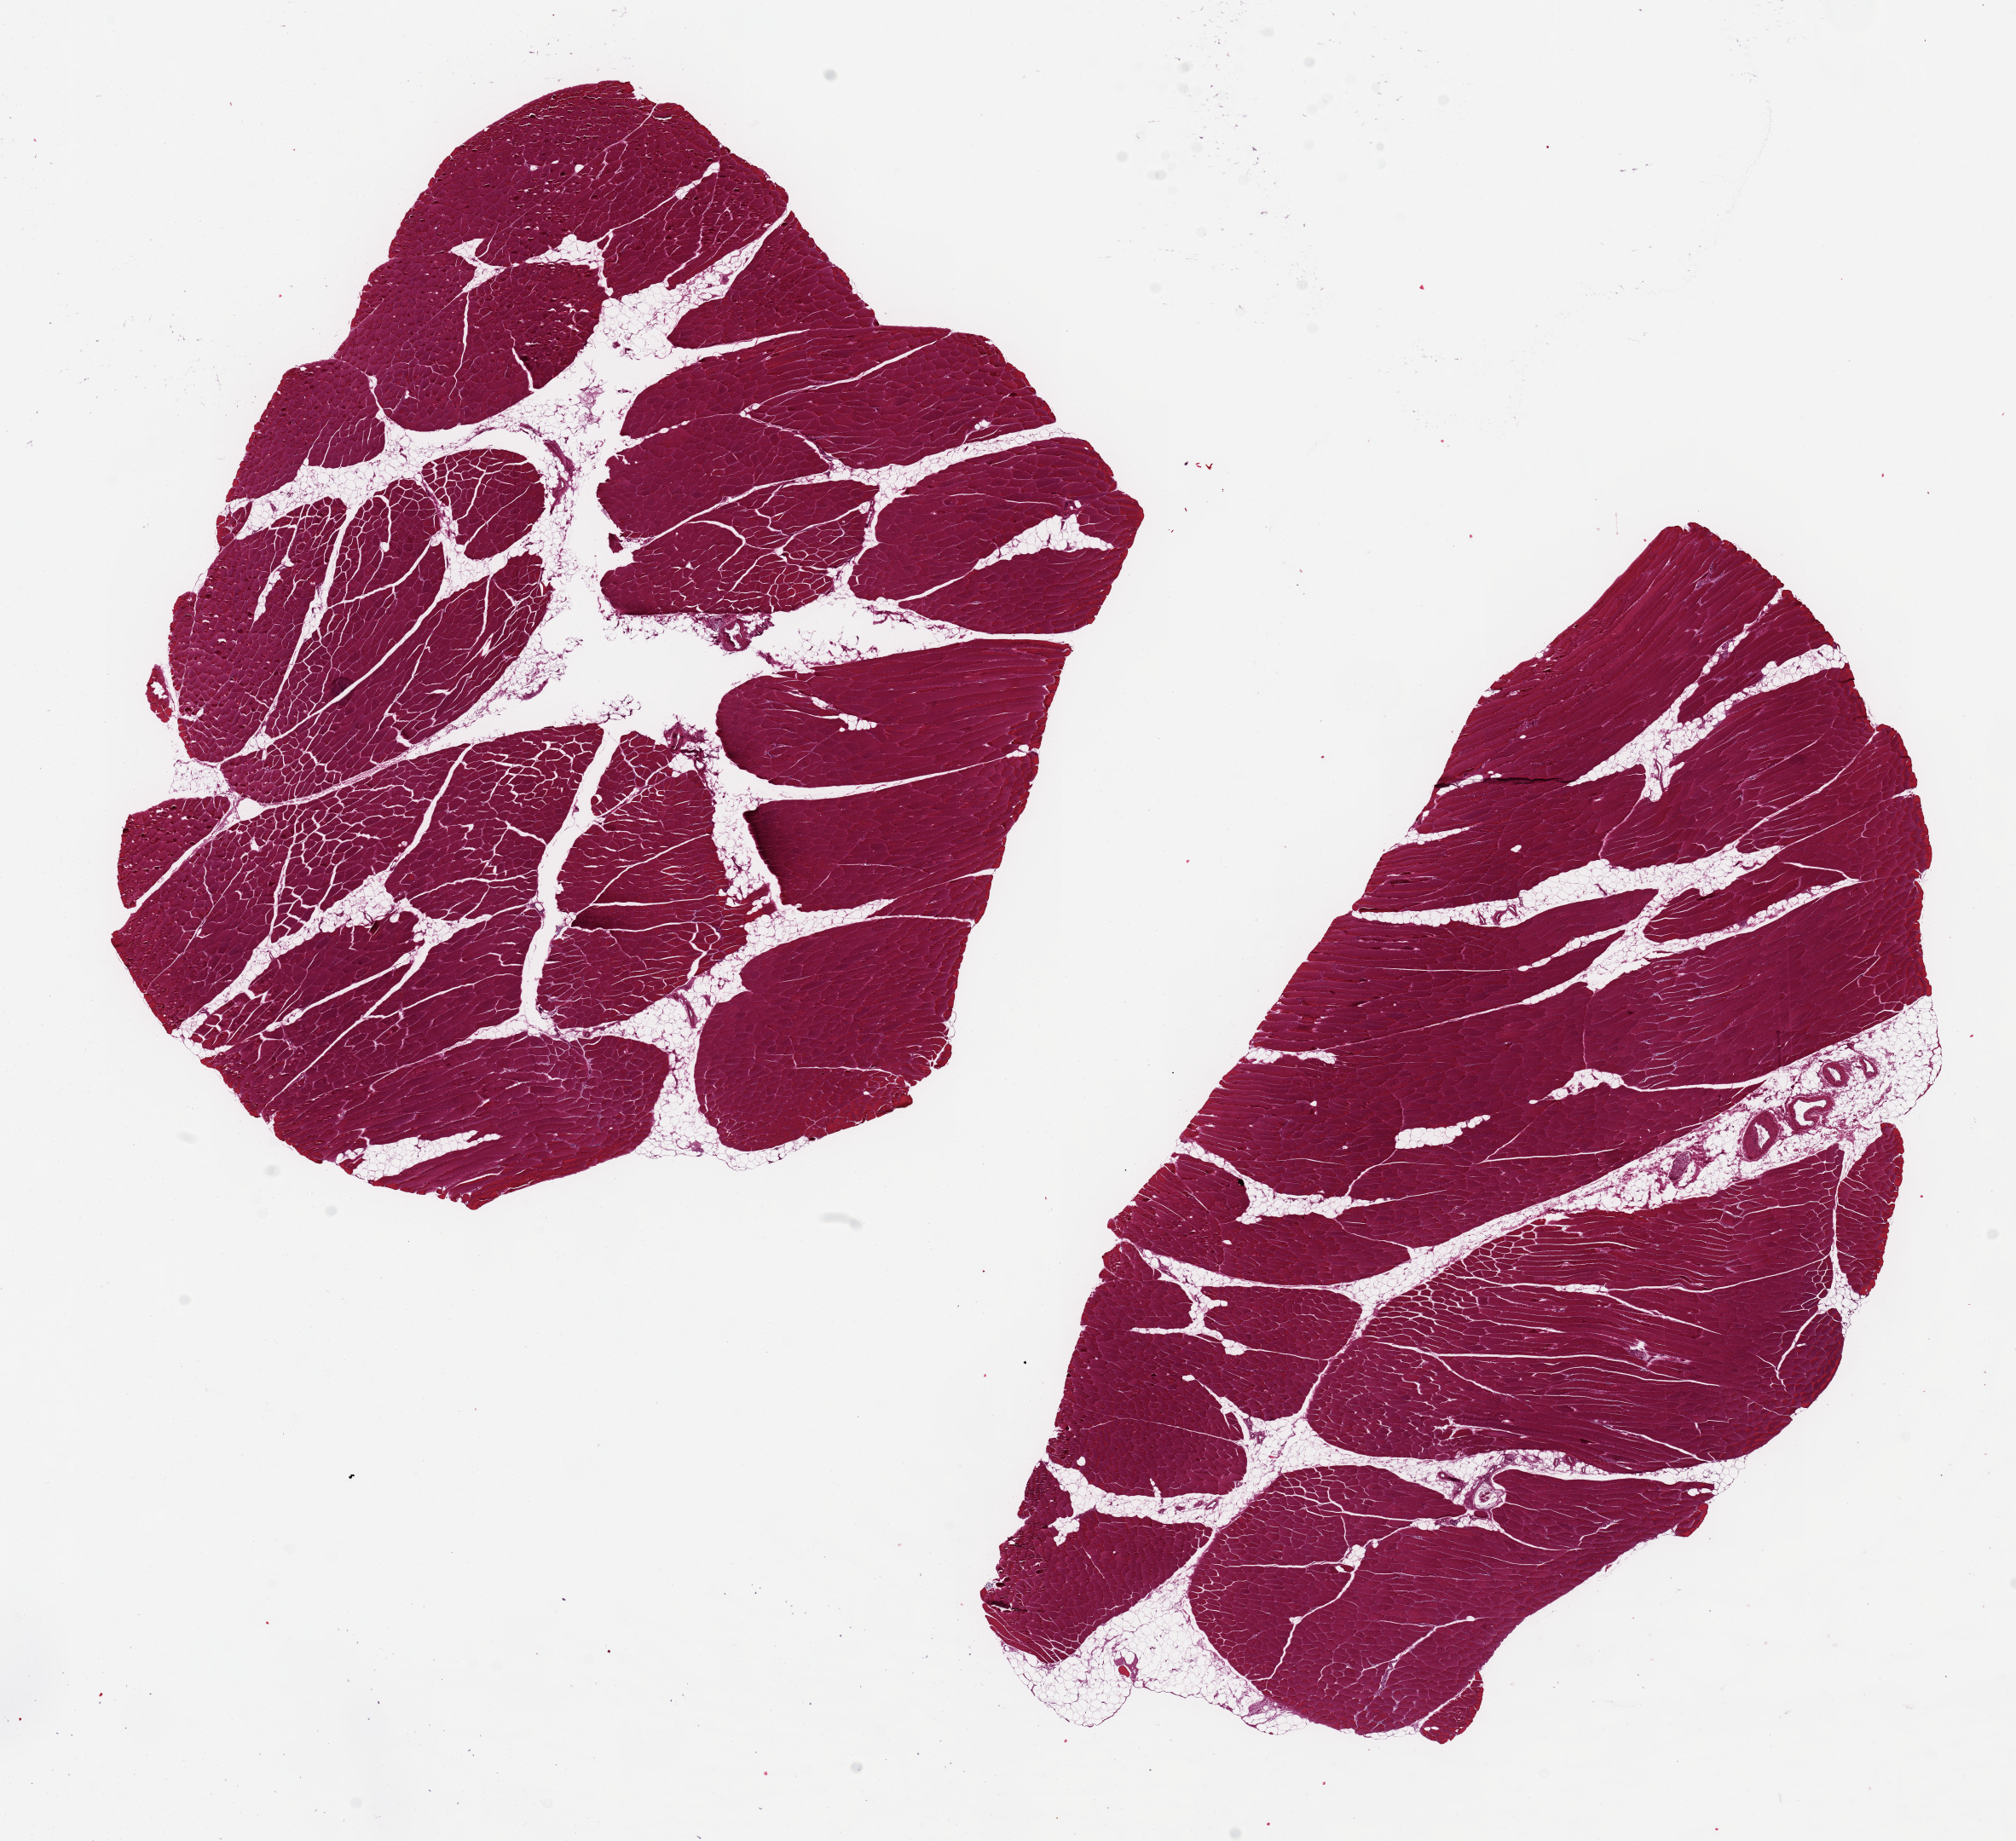
Haematoxylin and eosin whole-slide image, low-resolution overview of the scanned area, about 18.7 x 17.1 mm; PAXgene-fixed, paraffin-embedded tissue; section of skeletal muscle (target tissue); donor tissue sample.
* review note (as recorded): 2 ~ 10x7mm aliquots, ~15% interfascicular fat